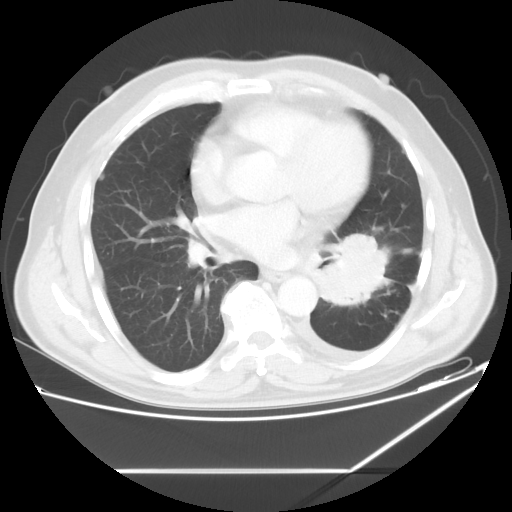
Chest CT, one axial slice. Position 29 of 60 along the scan axis. Reconstruction kernel STANDARD. 120 kVp. Lung window (W 1500 / L -600 HU). 5 mm slice thickness. 512 × 512 image matrix, field of view 395 × 395 mm. Male patient, age 62 years. Case-level facts recorded for this patient, not image findings: clinical TNM (as recorded): T3 N0 M1.
Outlined on this slice (bounding box drawn by a radiologist):
- lung tumour (recorded histology: adenocarcinoma): bounding box [x1, y1, x2, y2] px = [319, 230, 390, 303]
- lung tumour (recorded histology: adenocarcinoma): [322, 229, 387, 308]